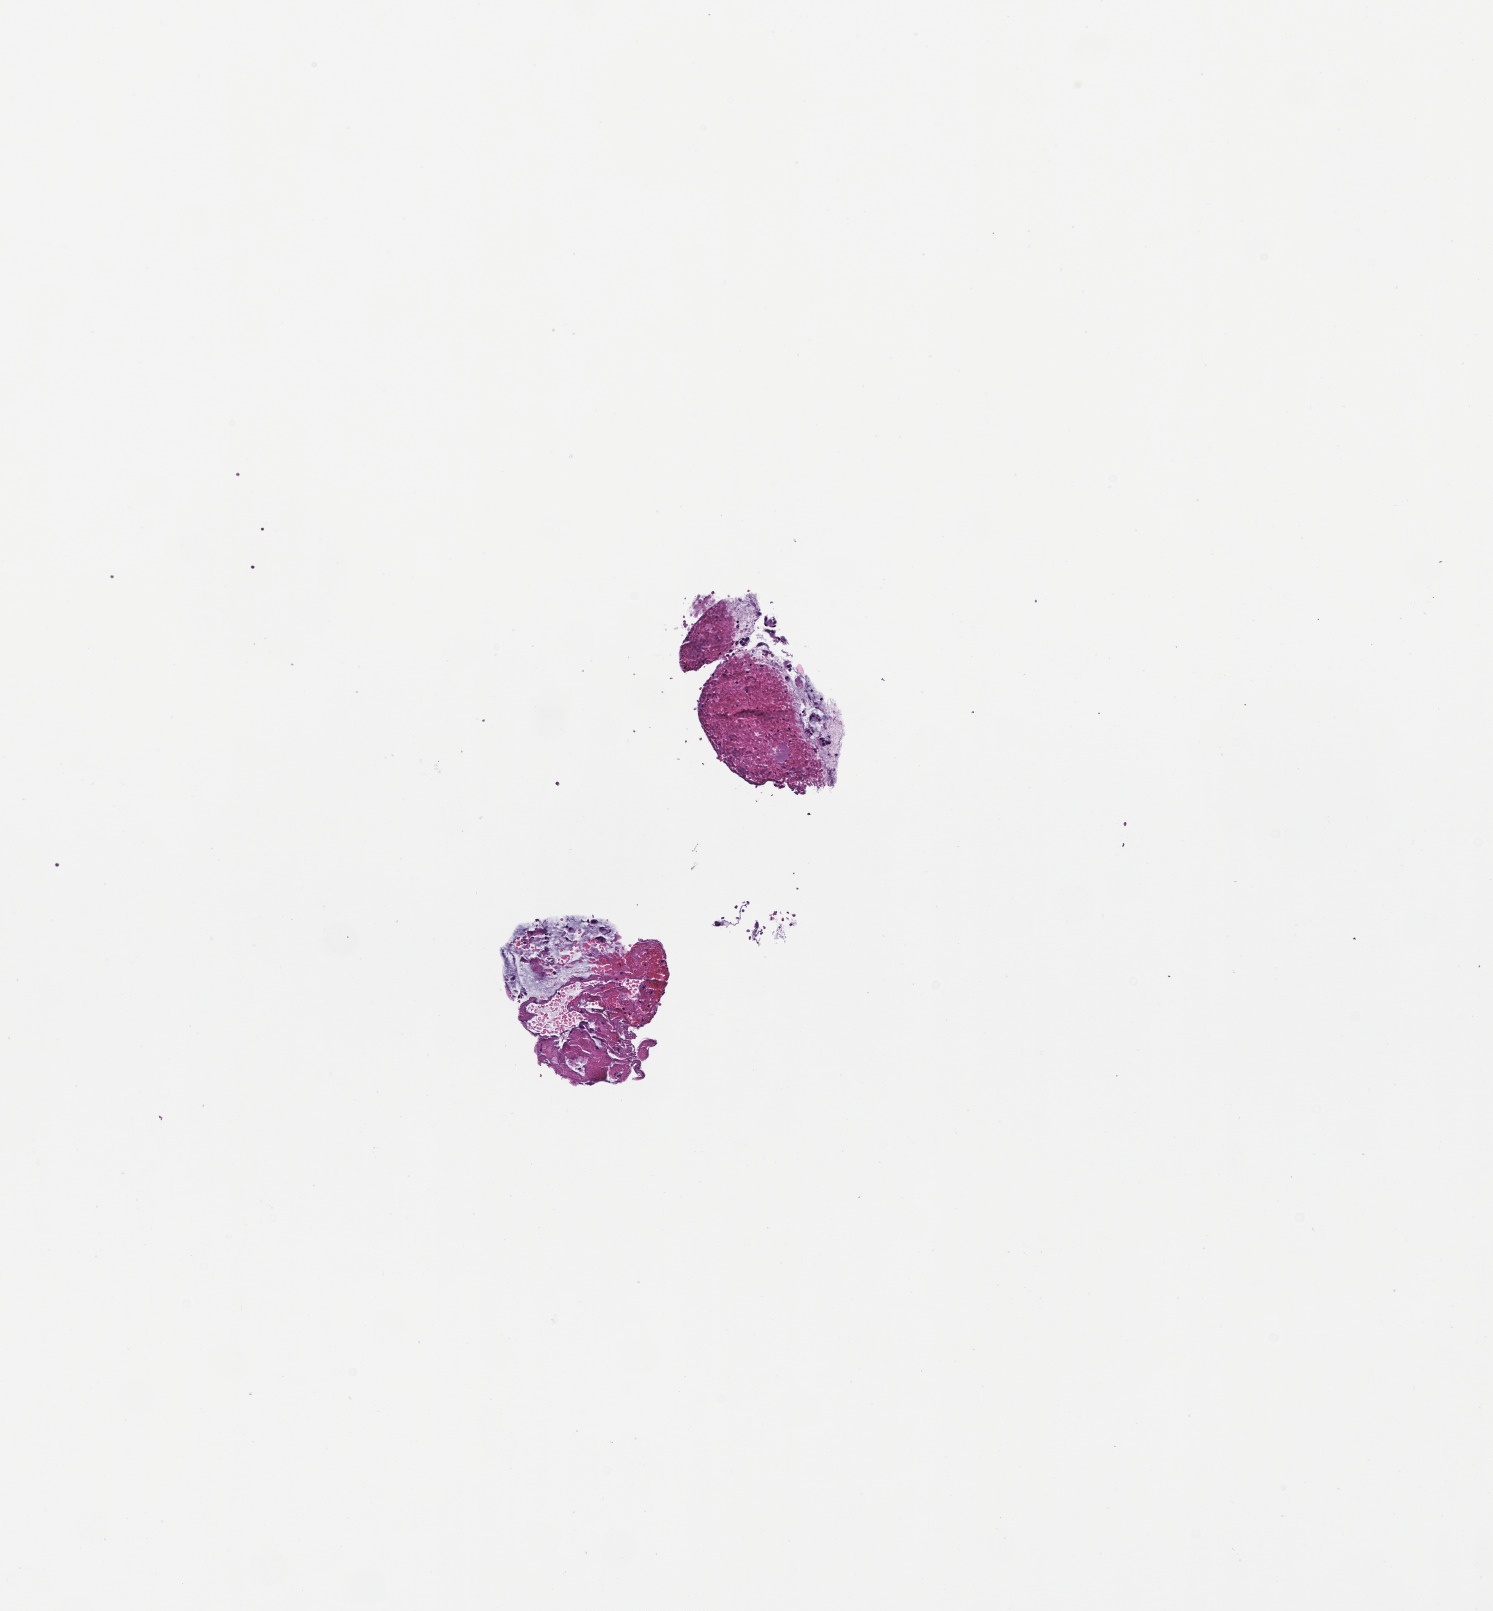
Whole-slide image, haematoxylin and eosin stain, low-resolution overview of the scanned area, about 3.0 x 3.3 mm. Formalin-fixed paraffin-embedded section. Site: lung. Collected at disease progression. Female patient.
This section: primary tumour tissue. Diagnosis: Non-Small Cell Lung Carcinoma.